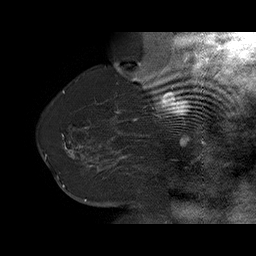
Breast MRI (dynamic contrast-enhanced), one sagittal slice. Position 51 of 75 along the scan axis. Dynamic contrast-enhanced series, time point 2 of 6 at this slice position (early post-contrast). 1.5 T. TE 4.5 ms, TR 32.4 ms. 256 × 256 image matrix. Female patient. From the clinical record (not read from this slice): setting: breast cancer imaged before/during neoadjuvant chemotherapy; receptor status: HR-positive, HER2-negative.
Outlined on this slice (semi-automatically segmented with operator editing):
- analysis volume of interest (the breast-tissue region the enhancement analysis was run in; not a lesion): bounding box (x1, y1, x2, y2) in pixels: (58, 134, 166, 191)
- tumour enhancement mask (voxels above the 100 % enhancement threshold inside the analysis volume of interest): (62, 135, 127, 187)